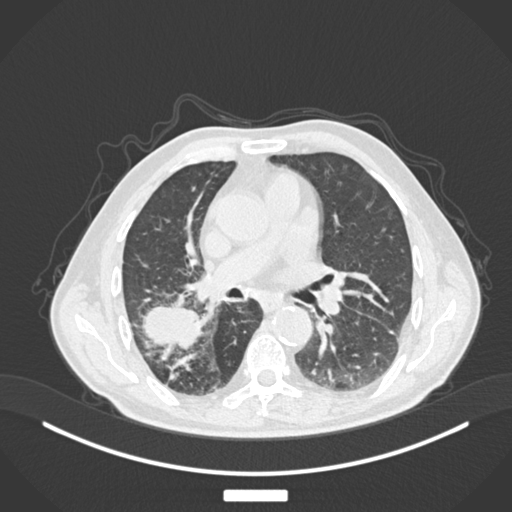
Chest CT, one axial slice; slice 92 of 201 in the series (ordered by position); reconstruction kernel B30f; 120 kVp; lung window (W 1500 / L -600 HU); 1 mm slice thickness; 512 × 512 image matrix, field of view 400 × 400 mm. Patient: male, 72 years. From the clinical record (not read from this slice): clinical TNM (as recorded): T3 N2 M0.
Annotated regions visible in this slice (bounding box drawn by a radiologist):
- lung tumour (recorded histology: adenocarcinoma): bounding box [x1, y1, x2, y2] px = [141, 302, 205, 354]